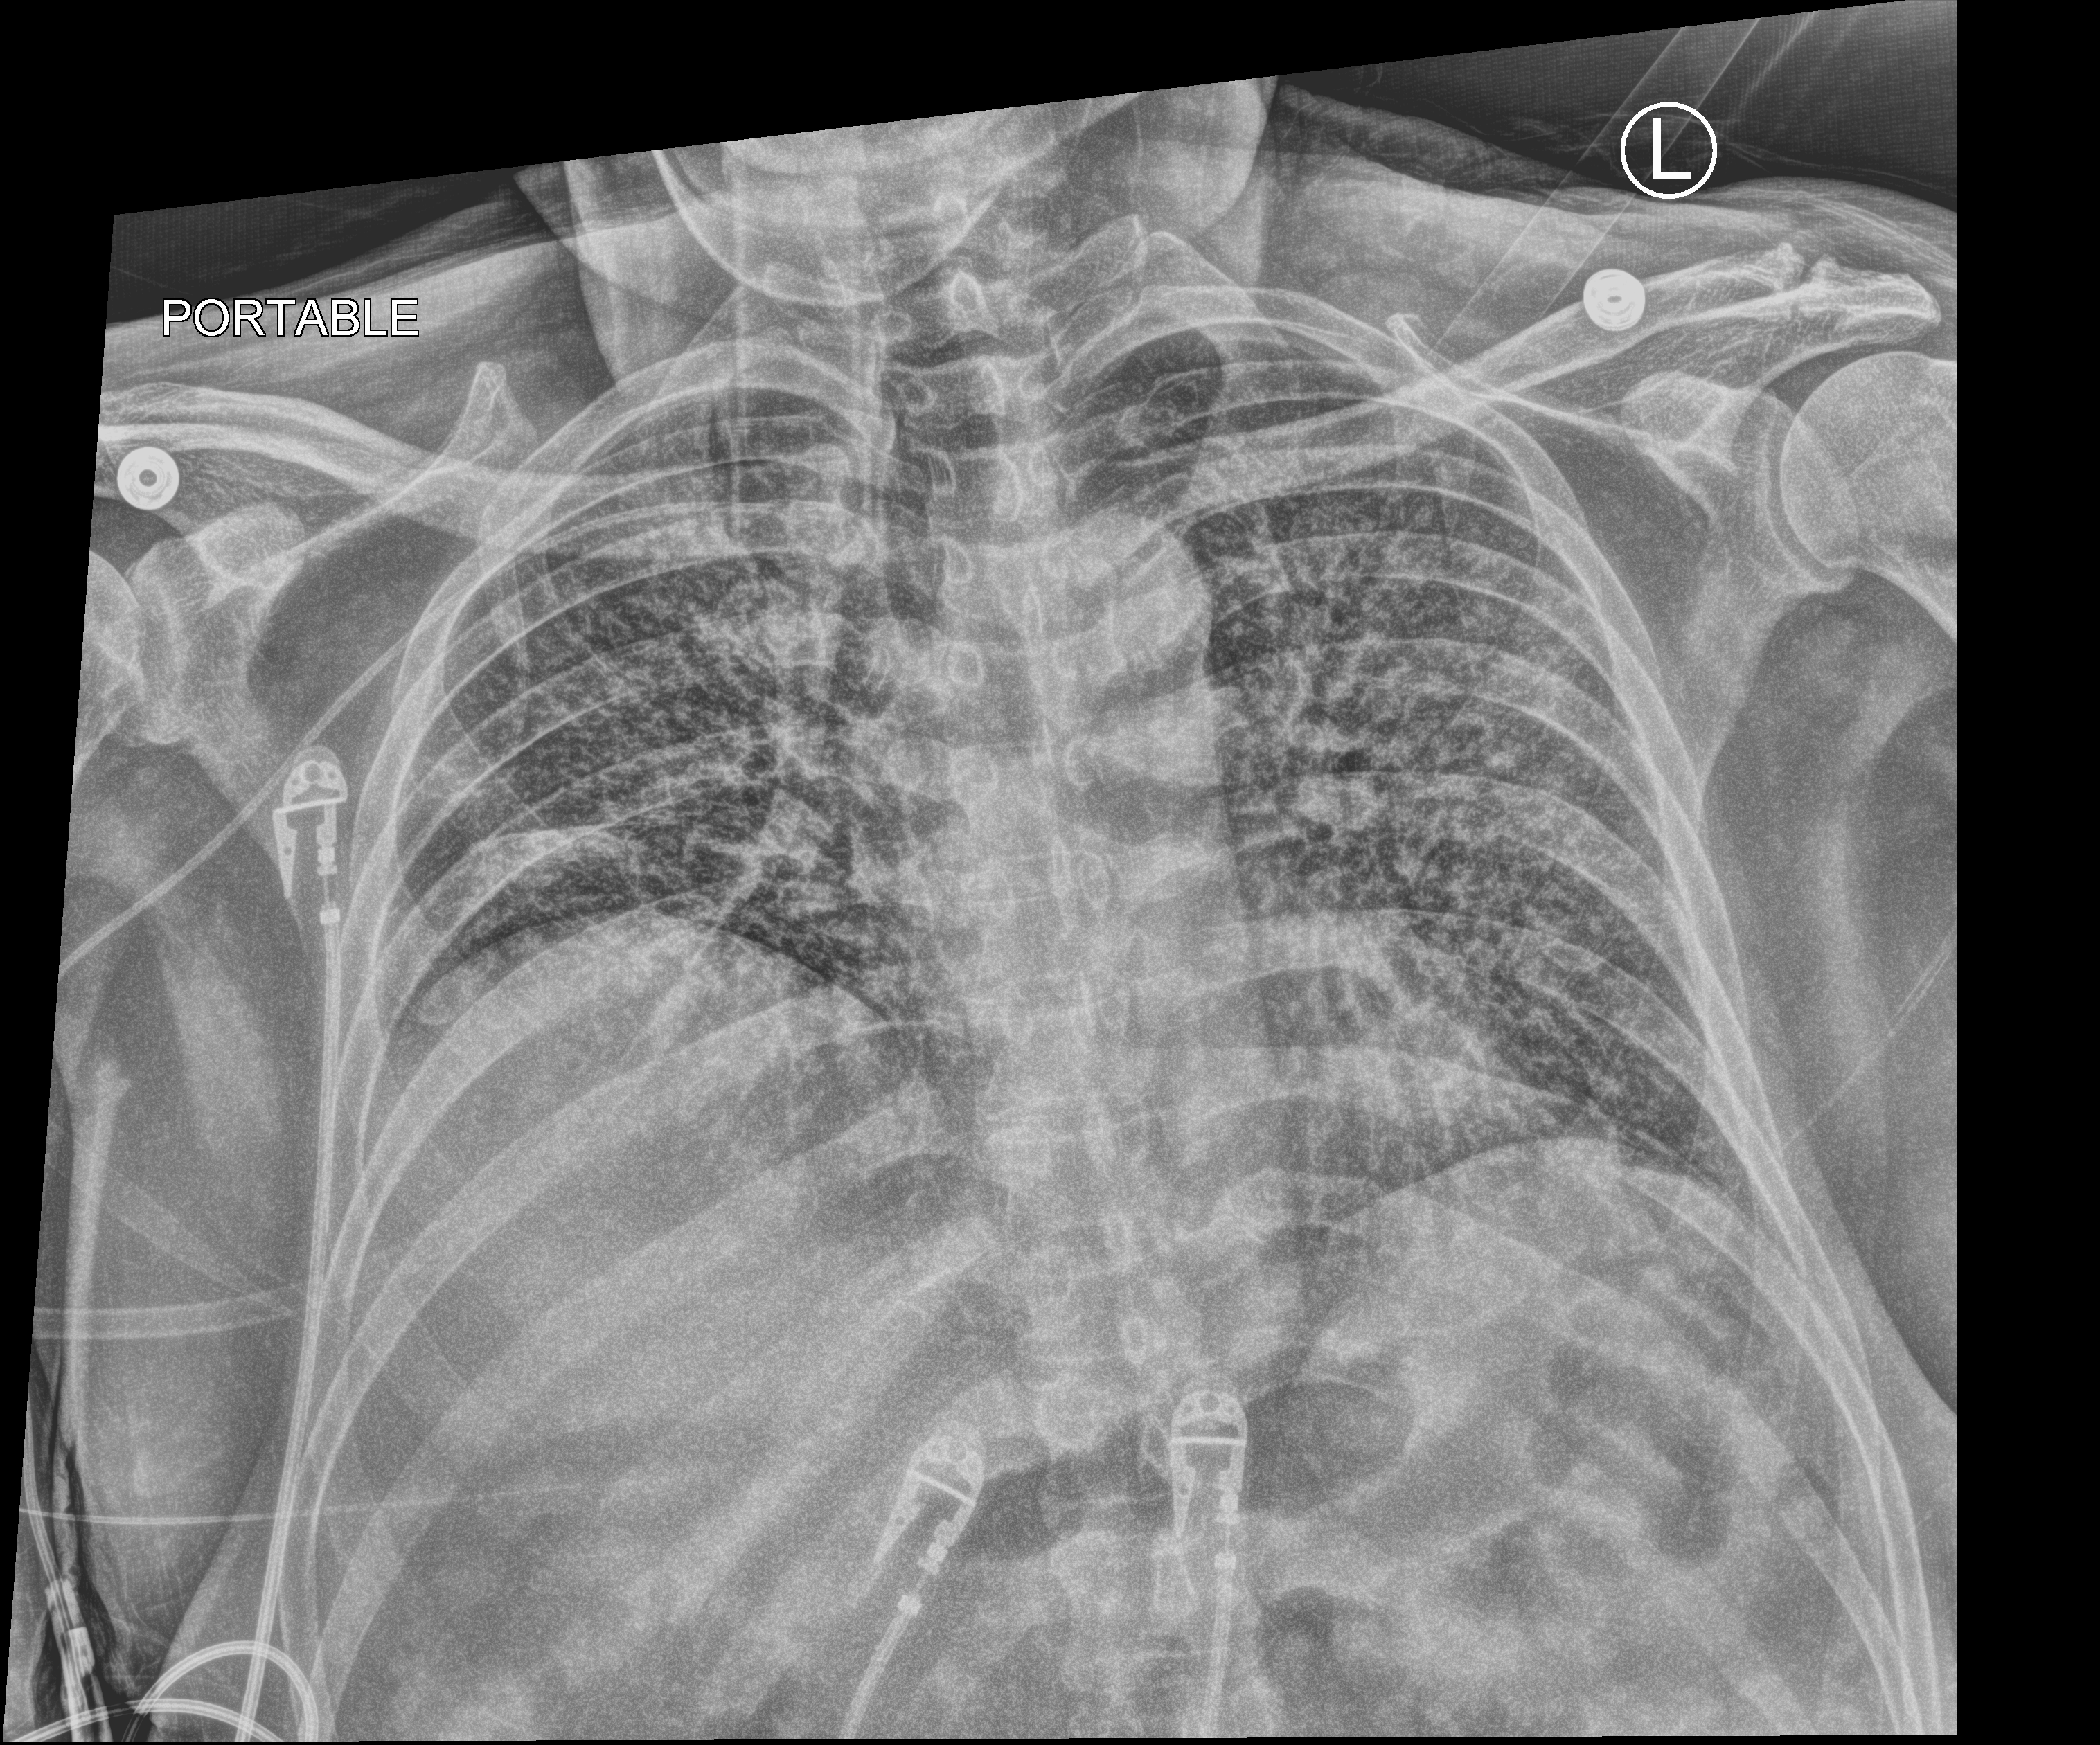
Chest X-ray (portable); anteroposterior (AP) projection. Male patient hospitalised with COVID-19, age 18–59 years.
Hospital-stay facts (about this admission, not read from this image; timing relative to this image not recorded):
- mechanically ventilated during this hospital stay: yes
- admitted to intensive care during this hospital stay: yes
- other chronic lung disease (admission record): no